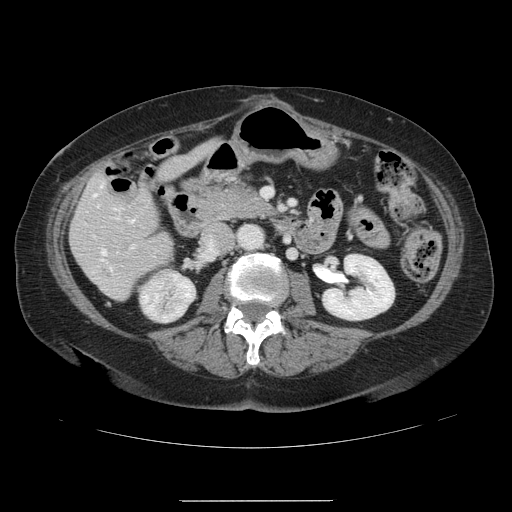
Contrast-enhanced abdominal CT, one axial slice; position 43 of 141 along the scan axis; 120 kVp; soft-tissue window (W 400 / L 40 HU); 512 × 512 image matrix, field of view 393 × 393 mm. Female patient, age 74 years. Case-level facts recorded for this patient, not image findings: diagnosis: colorectal cancer liver metastases, imaged before liver resection; multiple liver metastases: yes; largest metastasis: 7 cm; chemotherapy before resection: no.
Outlined on this slice (outlined manually by an expert reader):
- hepatic veins: bounding box <94,194,132,254> (left, top, right, bottom; pixels)
- liver: <71,142,216,299>
- planned liver remnant (the part of the liver to remain after resection): <71,142,216,291>
- portal vein (with intrahepatic branches): <113,207,134,248>